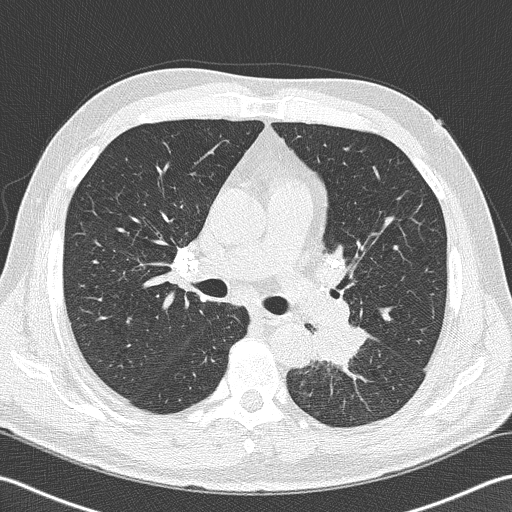
Low-dose screening chest CT, axial slice, second annual screen, lung window (W 1500 / L -600 HU), slice 66 of 170 in the series. Male, age 57 years at enrolment. Former smoker at enrolment.
Expert-annotated lung lesion, bounding box (x1, y1, x2, y2) in pixels: (294, 309, 374, 385). Screening reader's record for this exam (one nodule recorded; not confirmed to be the boxed lesion): non-calcified nodule or mass ≥4 mm, left lower lobe, 40 × 30 mm, spiculated (stellate) margins, soft tissue attenuation, pre-existing on the prior screen: no. Later outcome: lung cancer diagnosed 9 days after this screen — squamous cell carcinoma, NOS, left lower lobe, moderately differentiated (G2), stage IIIB (AJCC 6th edition), 38 mm at pathology.